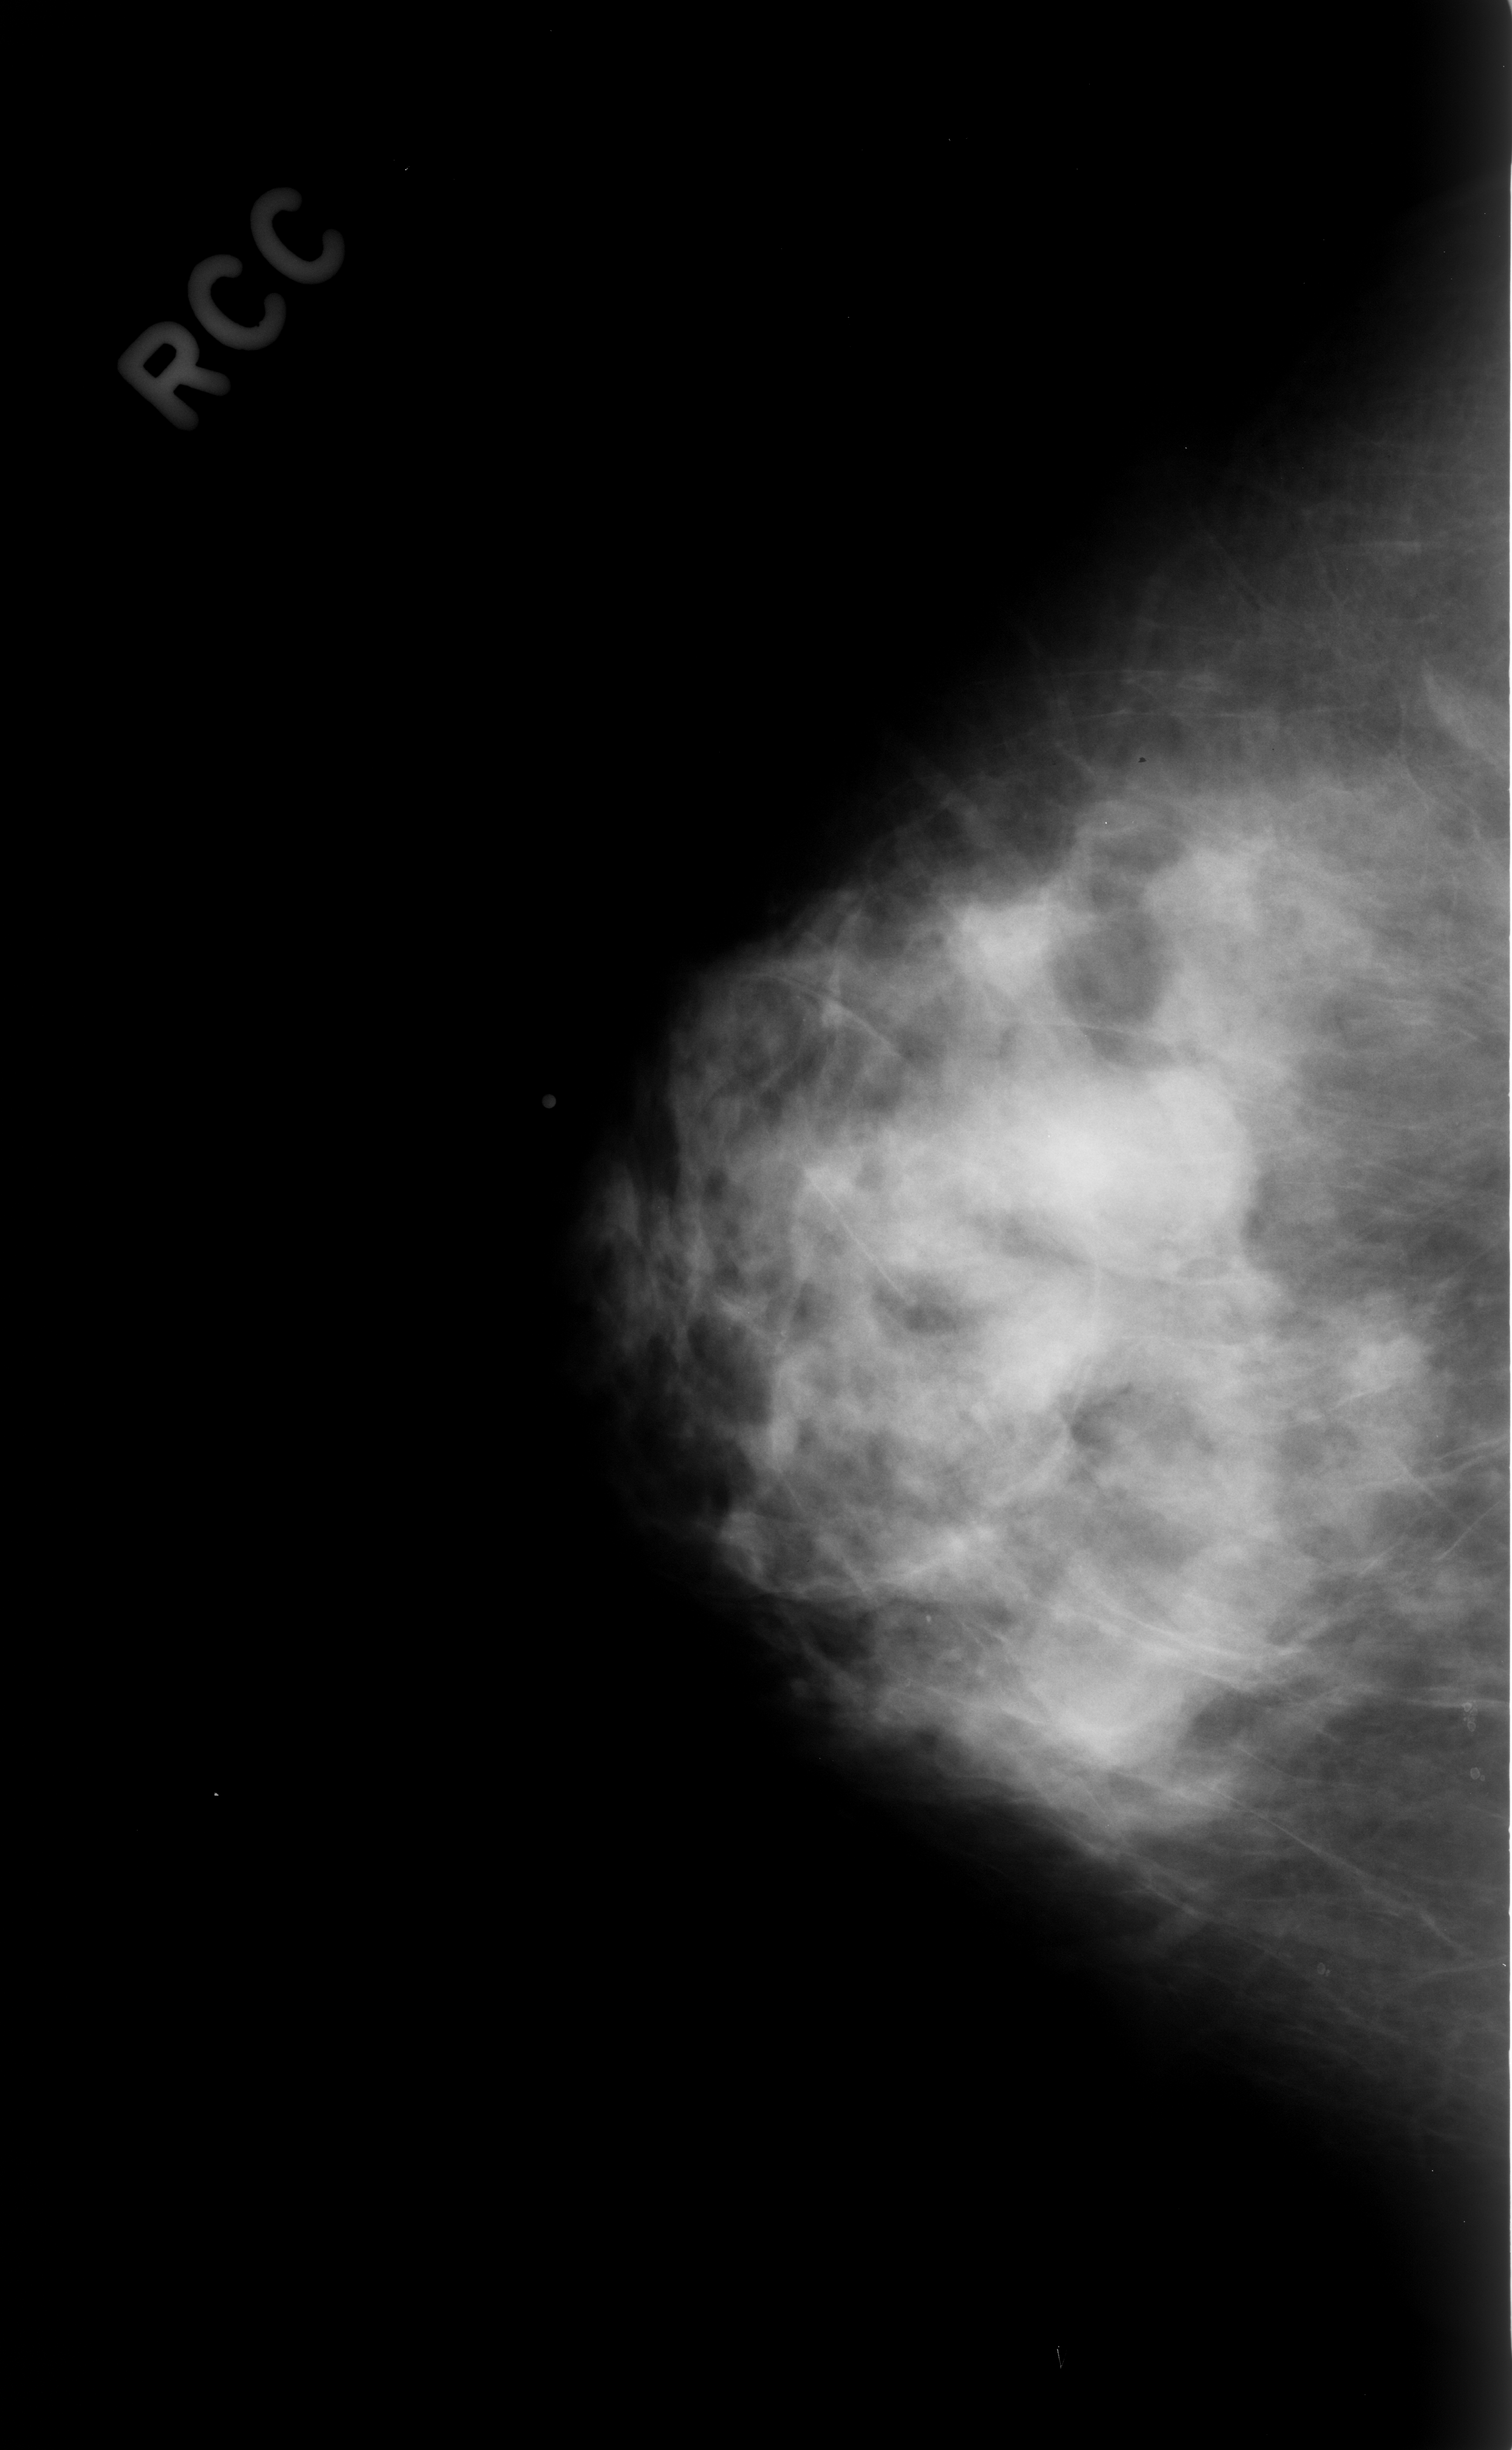
Digitized screen-film mammogram; right breast; CC view; 1512 × 2450 image matrix.
Expert-marked regions of interest on this image (one box per marked abnormality):
- mass, shape oval, margins obscured; BI-RADS assessment category 3; benign; no additional work-up was recommended (outcome (as recorded, no biopsy): benign without callback): box from (x=1008, y=1052) to (x=1265, y=1250) px